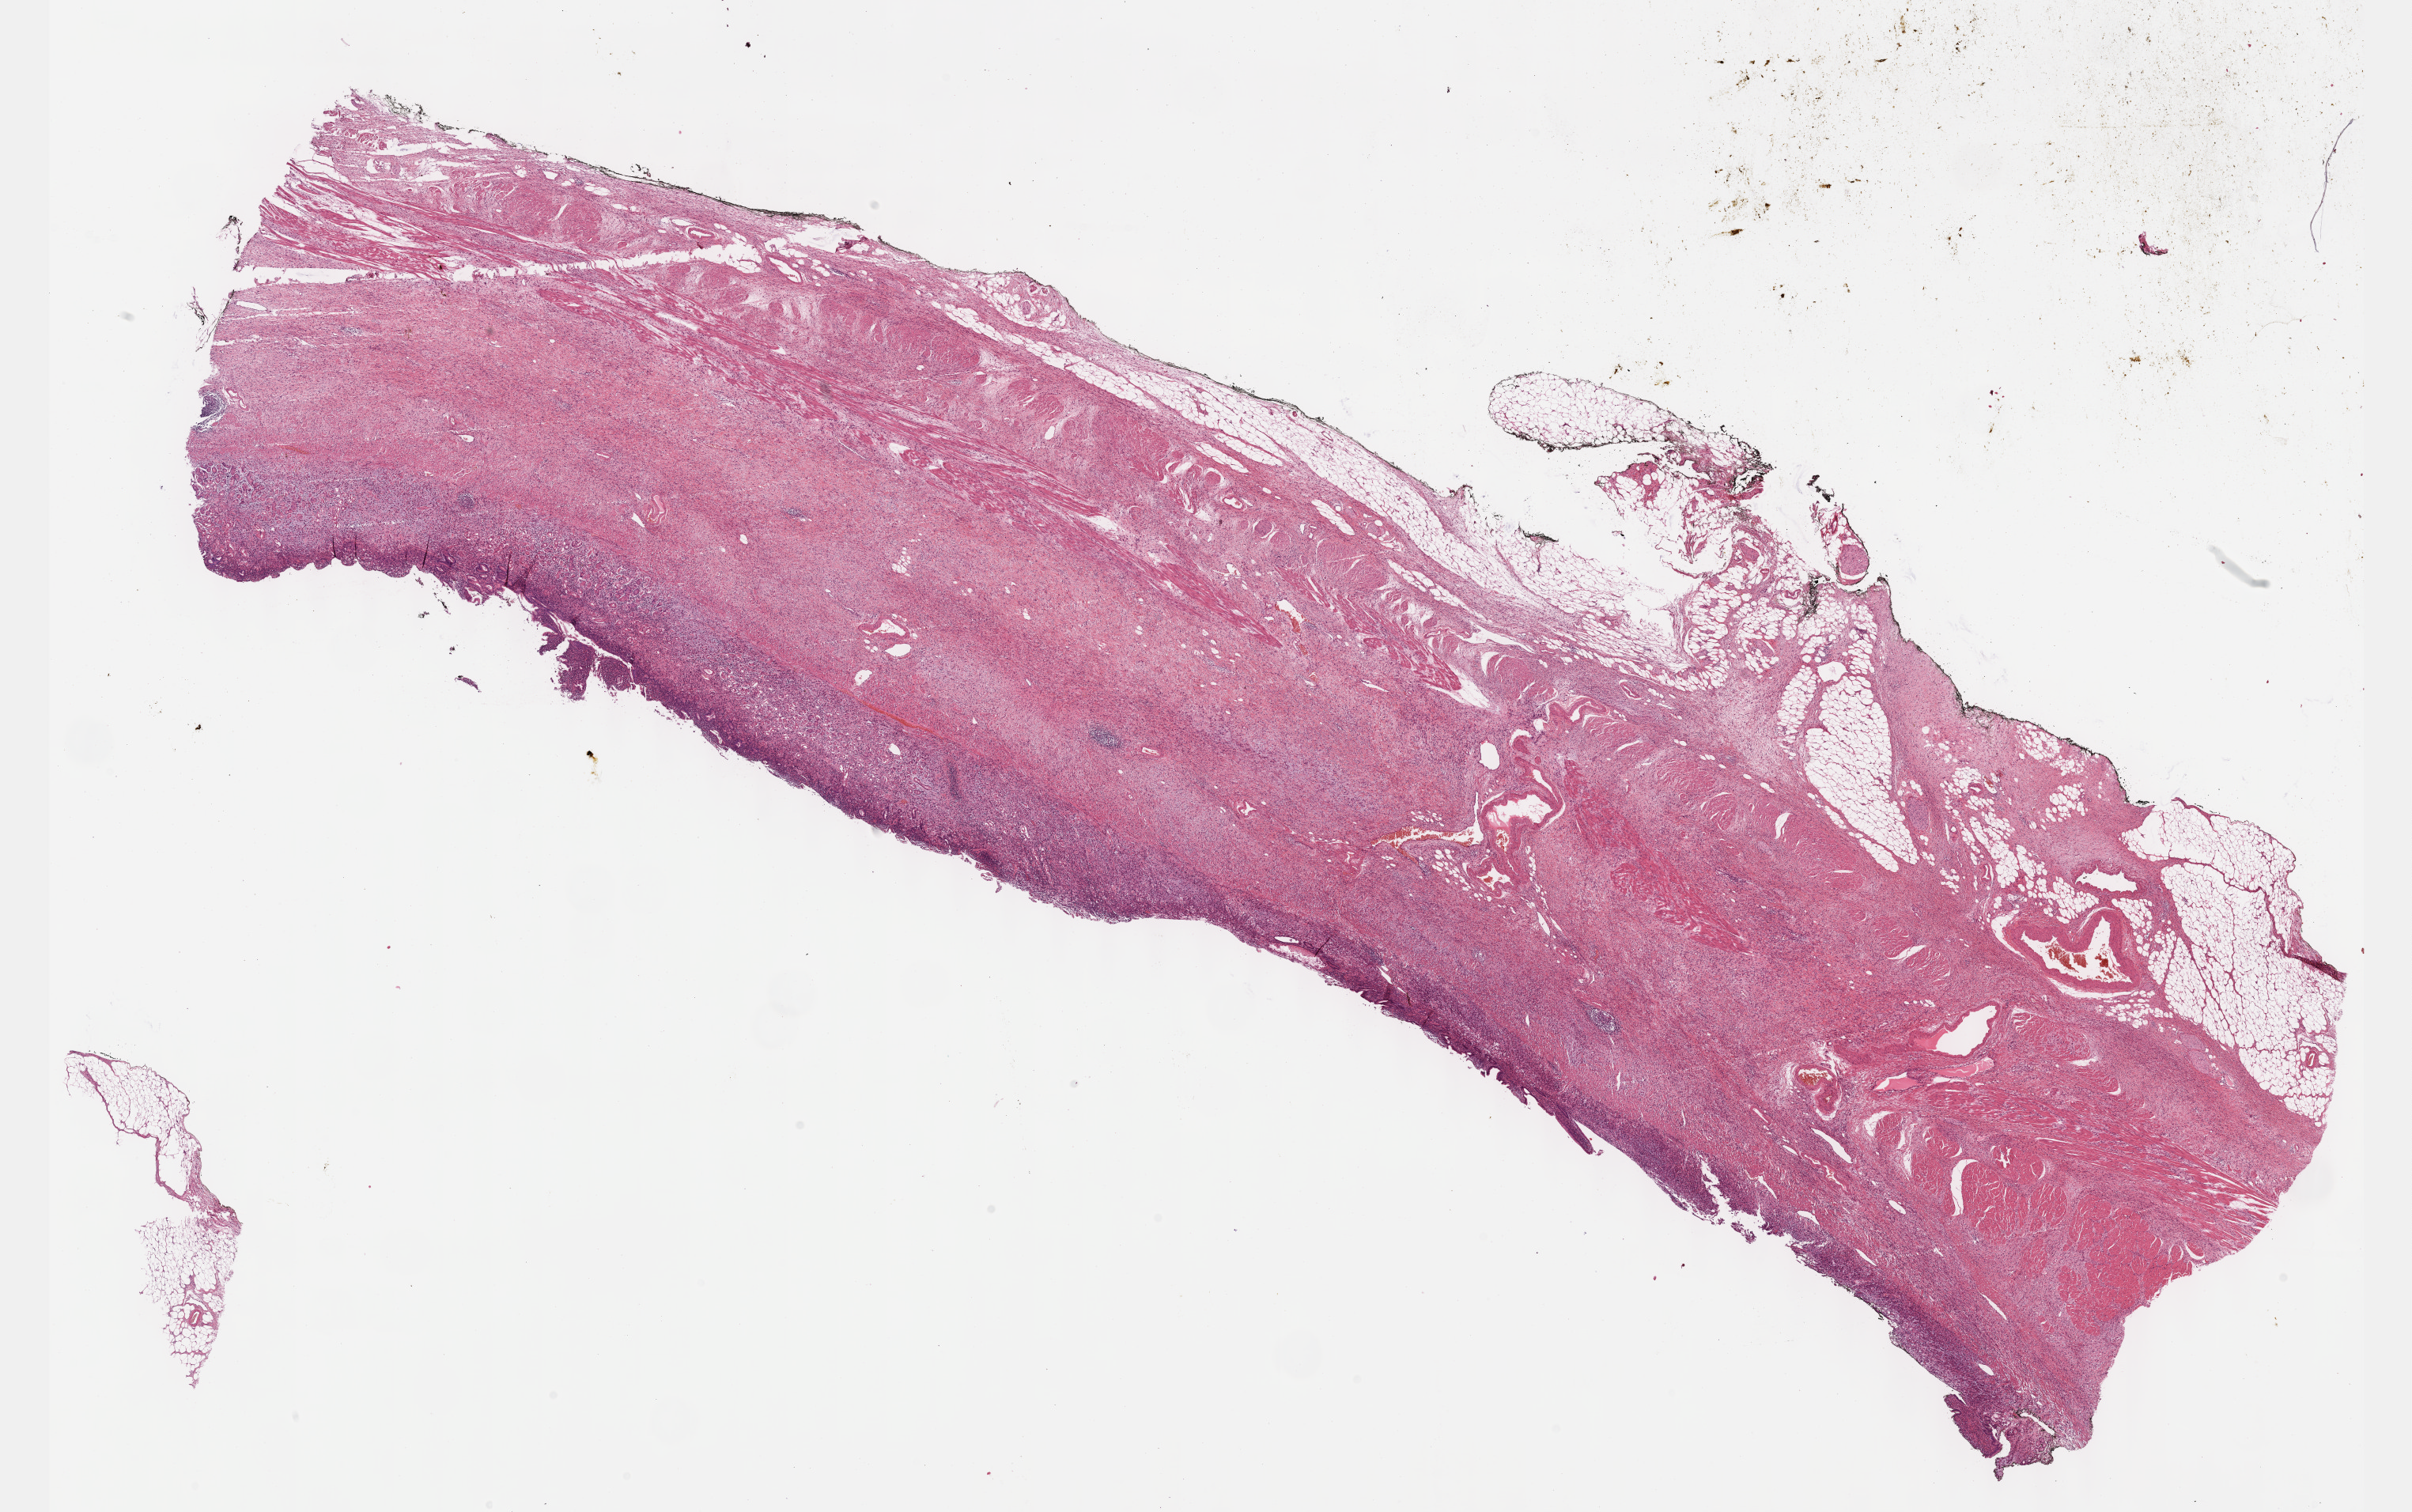
H&E whole-slide image — whole scanned area (about 24.6 x 15.5 mm) shown as a low-resolution overview. Formalin-fixed paraffin-embedded (FFPE) diagnostic section. Stomach, primary tumour sample. Female patient; age at initial diagnosis 56 years. Histologic grade: G3 (poorly differentiated).
Lymph nodes positive (case pathology): 0 of 68 examined. TNM: T3 N0 M0. AJCC pathologic stage: II (6th edition). Histologic diagnosis: Signet ring cell carcinoma (gastric antrum).